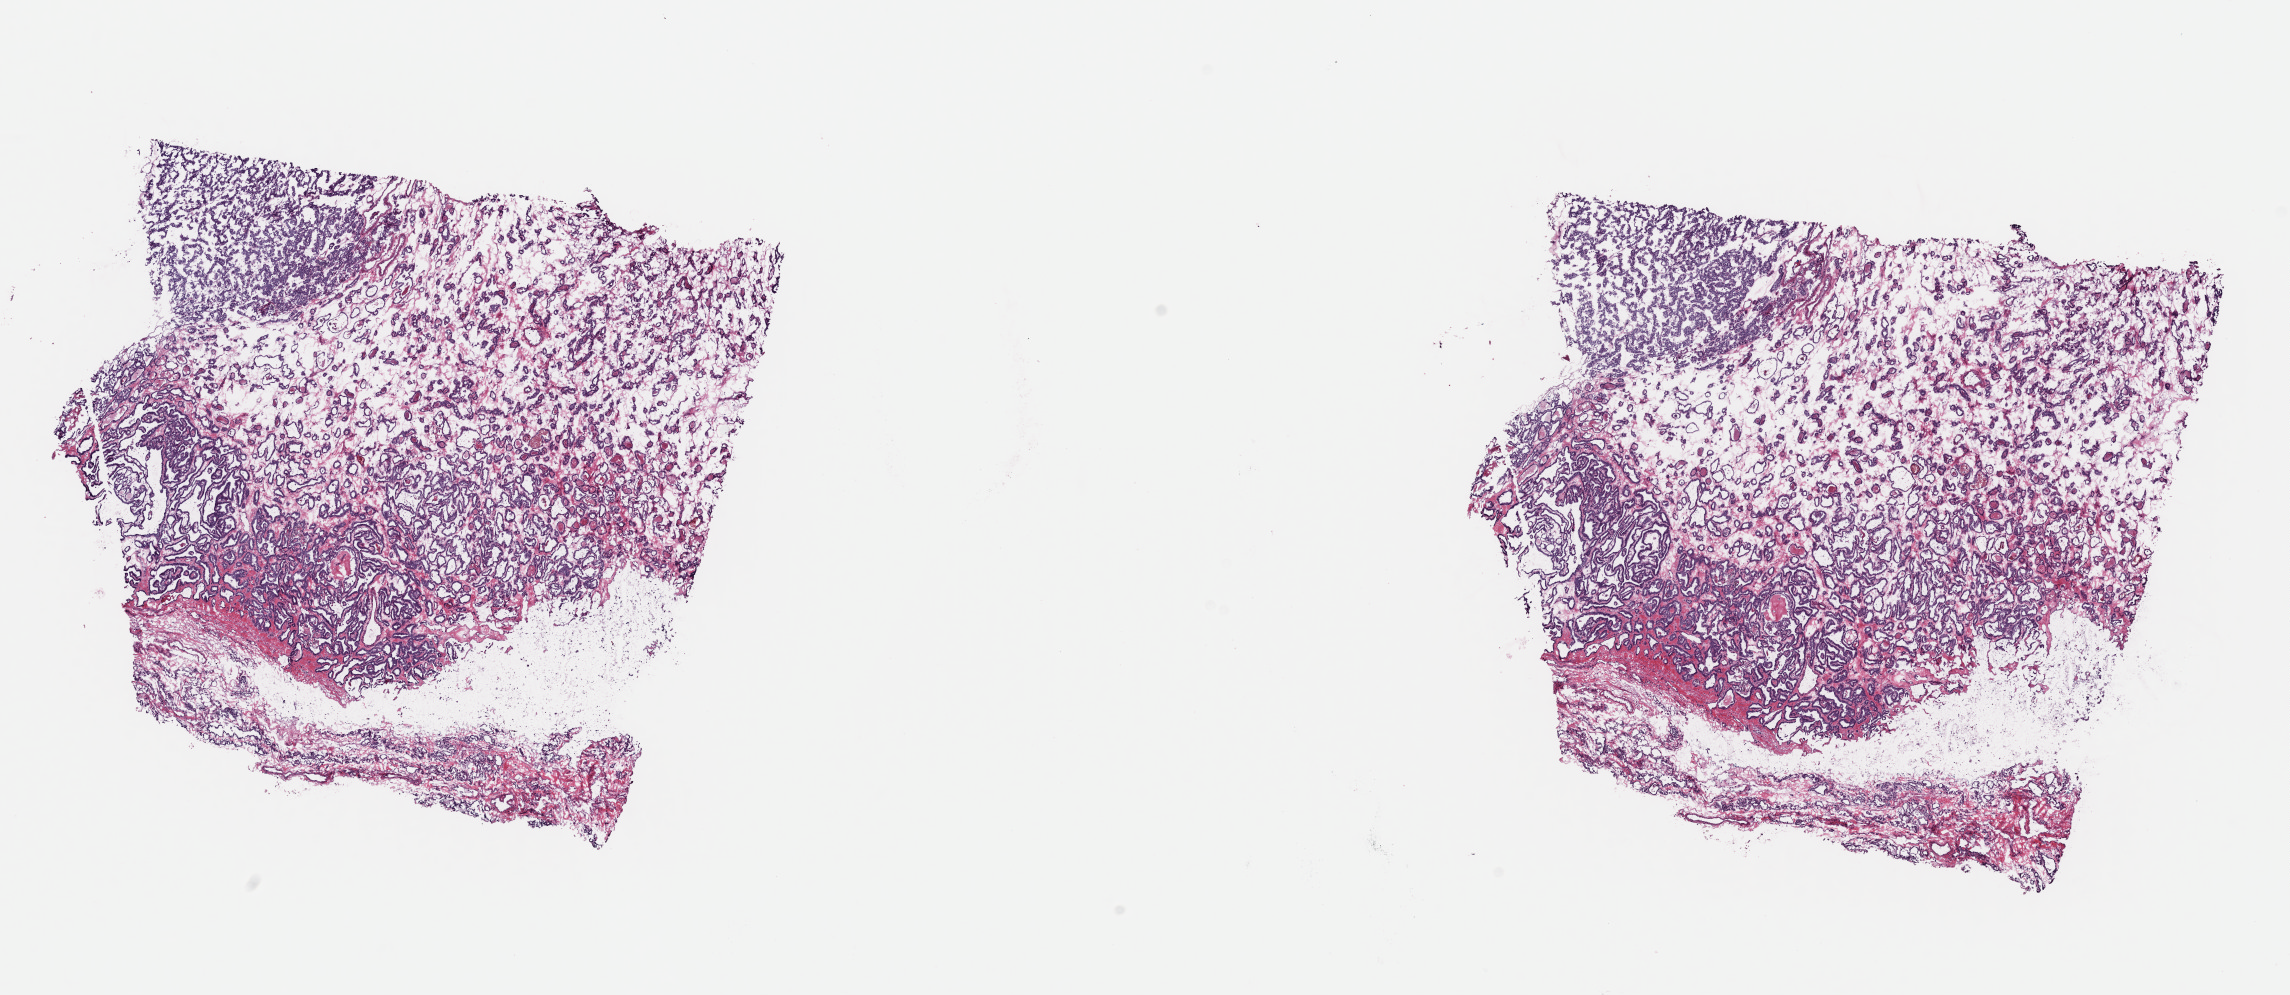
H&E-stained whole-slide image, low-resolution overview of the scanned area, about 18.1 x 7.9 mm (acquisition: 40x scan). Frozen section from the top of the tissue portion. Primary tumour sample from the thyroid. Female, age 61 years at initial diagnosis. Composition of this section per pathologist review: tumour cells 85%, tumour nuclei 80%, normal cells 15%, stromal cells 0%, necrosis 0%. Infiltration values recorded for this section: lymphocyte infiltration 0%, monocyte infiltration 0%, neutrophil infiltration 0%.
Histologic diagnosis: Papillary adenocarcinoma, NOS. AJCC pathologic stage: II (6th edition). Laterality: right.